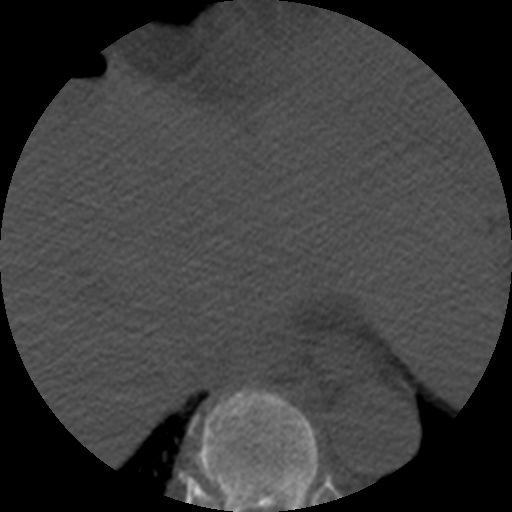
CT including the spine, one axial slice; position 297 of 508 along the scan axis; reconstruction kernel STANDARD; bone window (W 1800 / L 400 HU); 512 × 512 image matrix, field of view 160 × 160 mm. Patient age 57 years. Case-level facts recorded for this patient, not image findings: primary cancer: prostate.
Structures marked on this image (semi-automatic segmentation, software-assisted and operator-edited):
- T9 vertebra: bounding box [x1, y1, x2, y2] px = [192, 388, 319, 512]